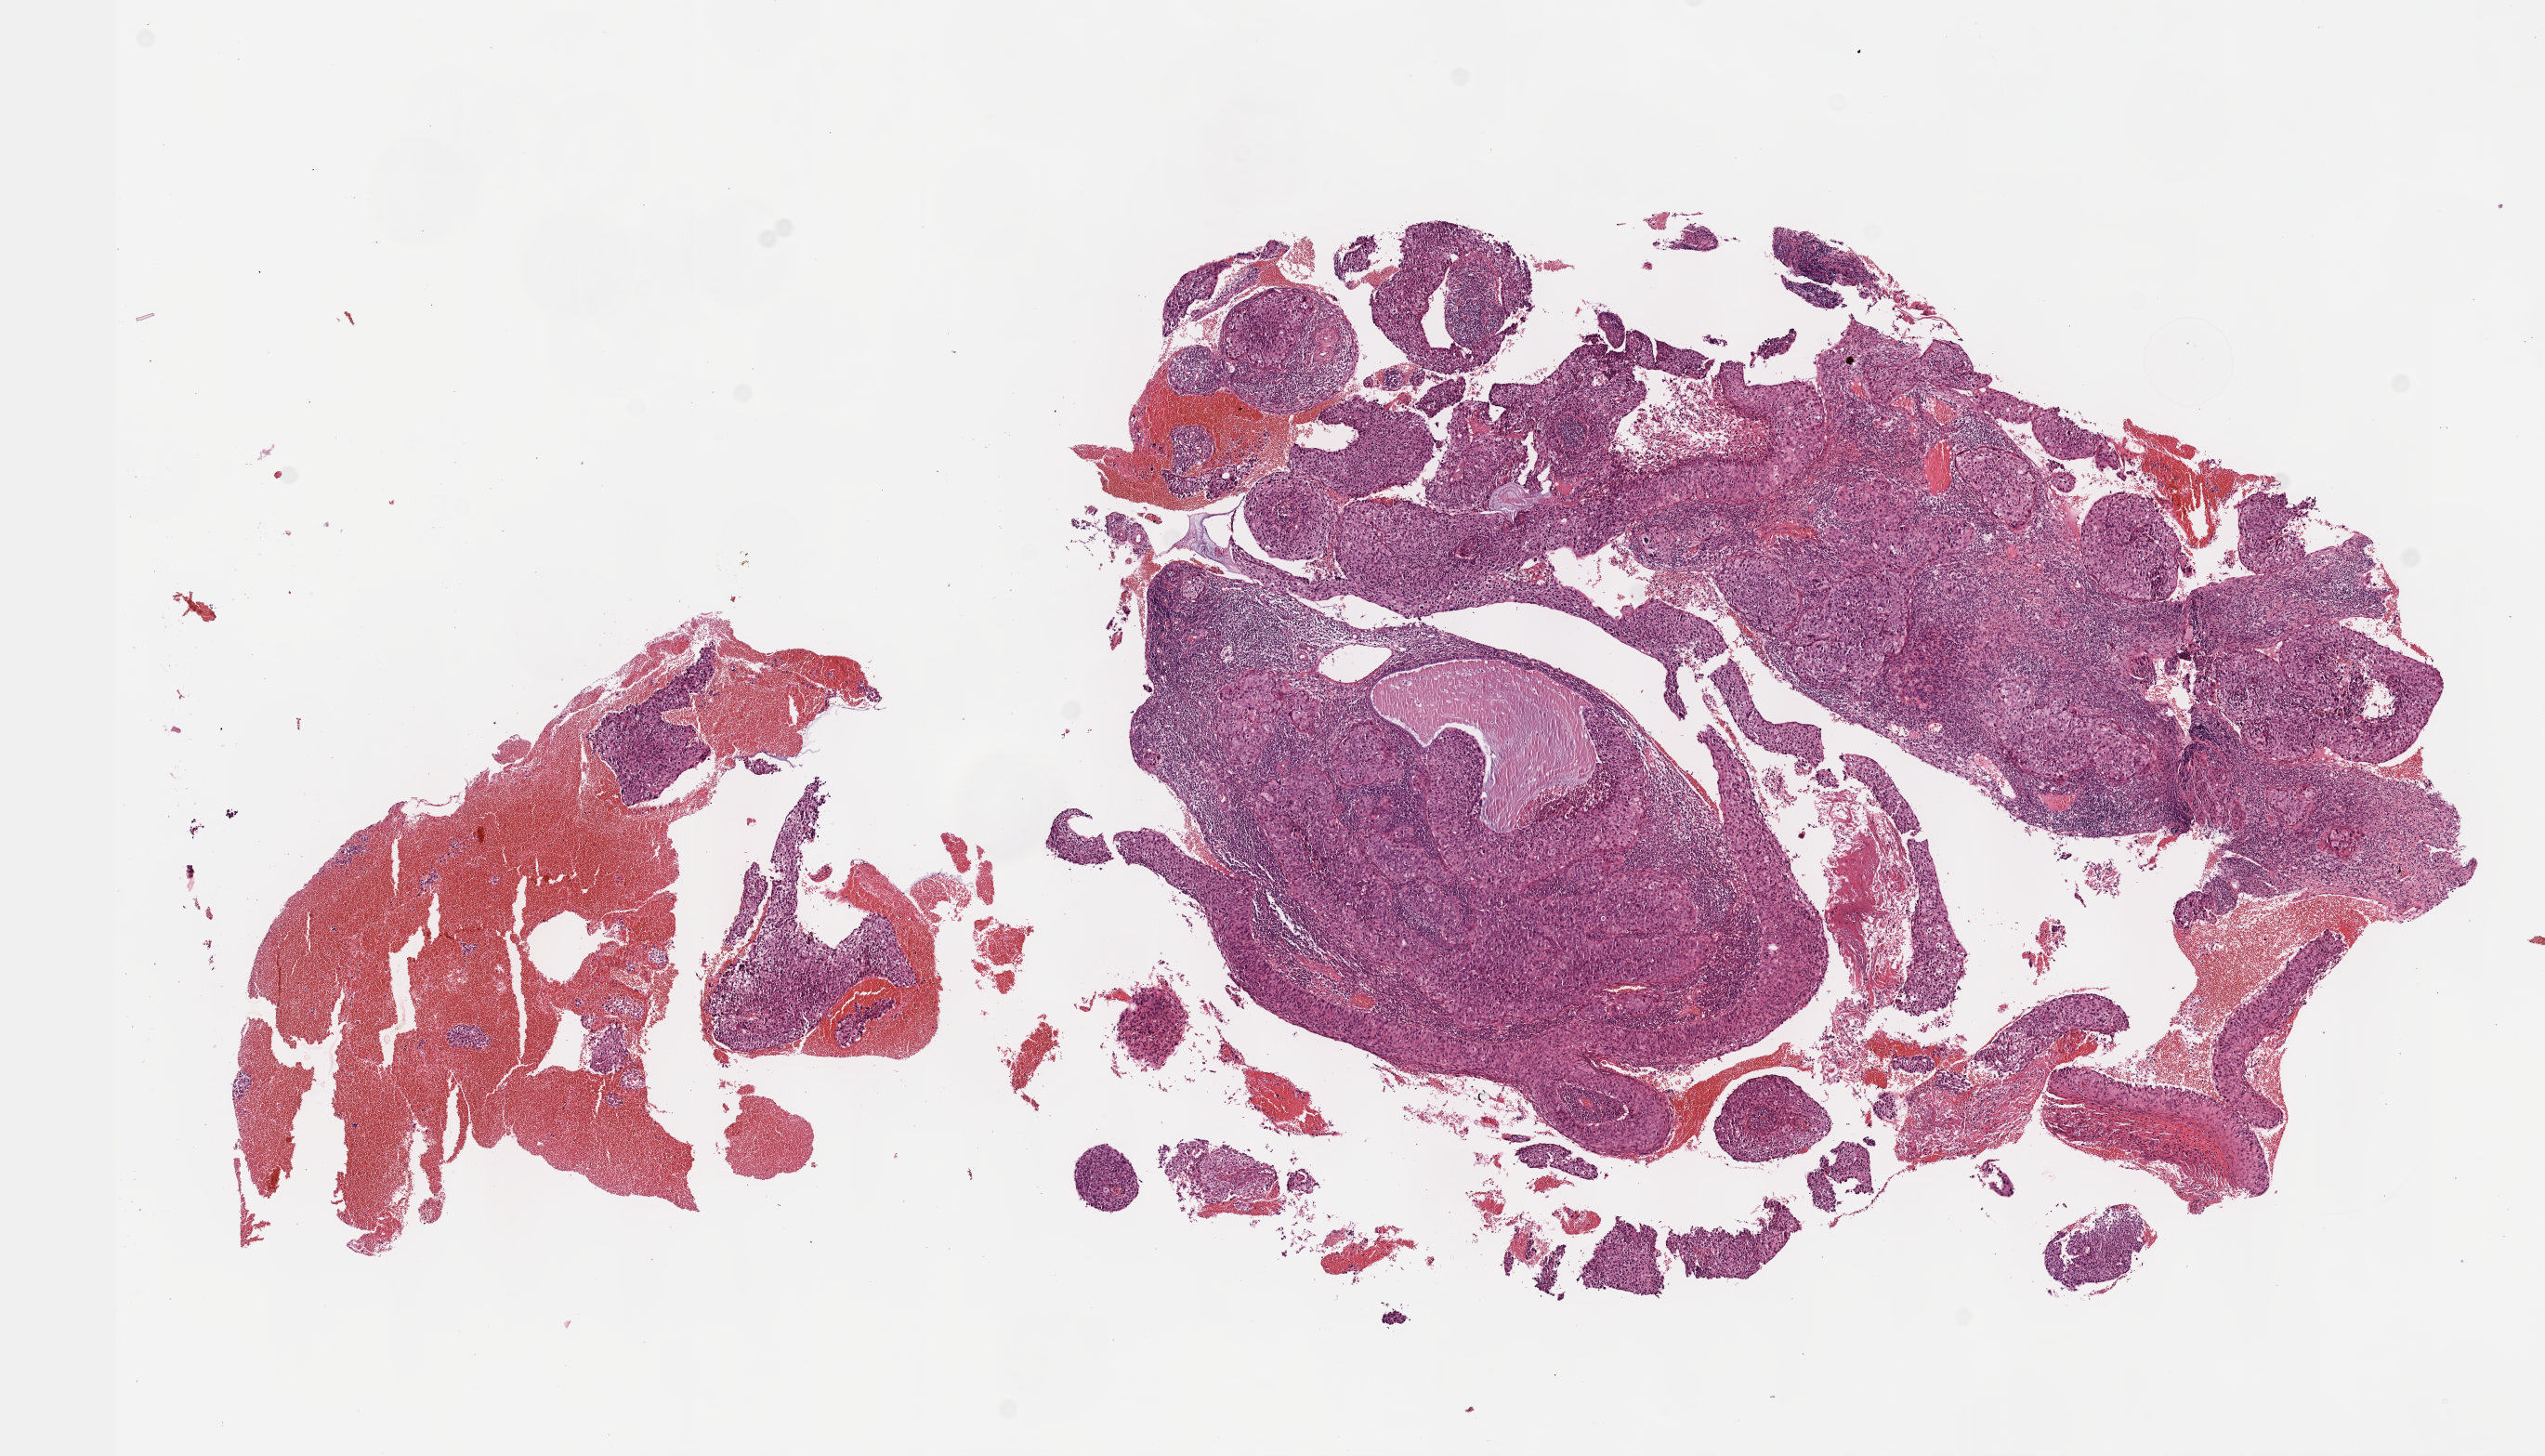
Digitized Hematoxylin and eosin (H&E) stained tissue section (whole slide) — a low-resolution overview of the entire scanned area, about 11.1 x 6.3 mm (slide scanned at 40x). Formalin-fixed paraffin-embedded (FFPE) diagnostic section. Cervix, primary tumour sample. Patient: female, age at initial diagnosis 42 years. Histologic grade: G2 (moderately differentiated).
FIGO stage: IIB. Diagnosis: Squamous cell carcinoma, NOS.